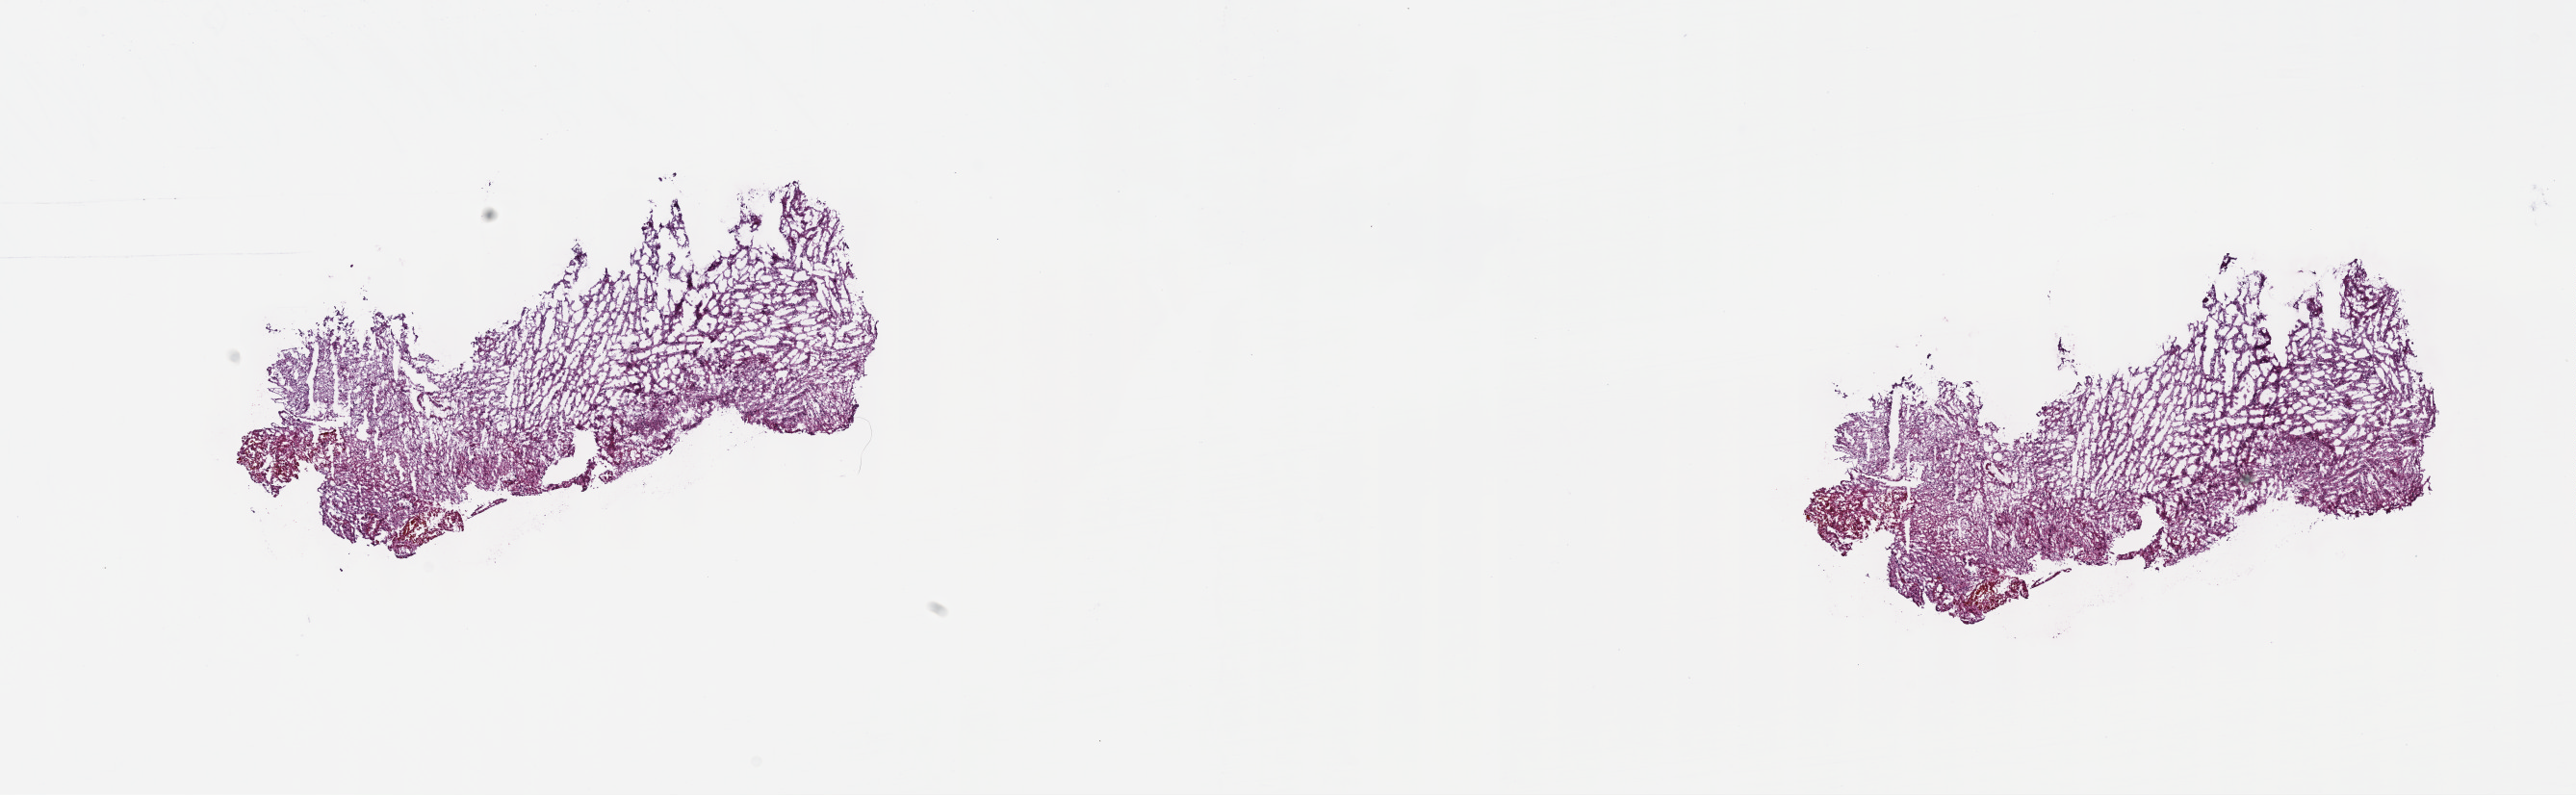
H&E-stained whole-slide image — shown as a low-resolution overview of the whole scanned area (about 21.6 x 6.7 mm, acquisition: 40x scan). Frozen section. Sample: primary tumour, brain. Male, age 66 years at initial diagnosis. Histologic grade: G3 (poorly differentiated). Pathologist review of this section (percent, as recorded): tumour cells 40%, tumour nuclei 80%, normal cells 10%, stromal cells 50%, necrosis 0%. Infiltration values recorded for this section: lymphocyte infiltration 0%, monocyte infiltration 0%, neutrophil infiltration 0%.
Laterality: left. Histologic diagnosis: Astrocytoma, anaplastic.